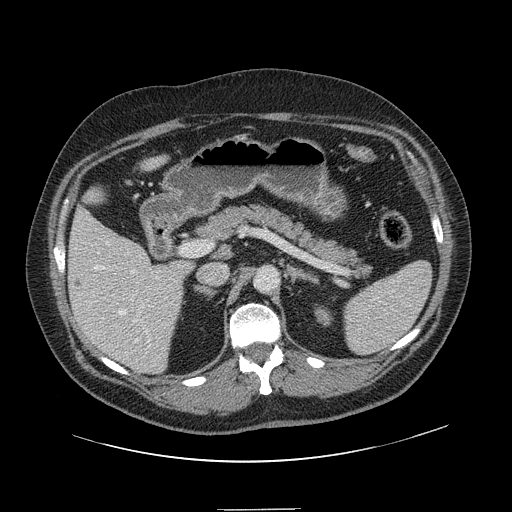
Contrast-enhanced abdominal CT, one axial slice; slice 76 of 154 in the series (ordered by position); intravenous contrast given; soft-tissue window (W 400 / L 40 HU); 512 × 512 image matrix, field of view 451 × 451 mm. Male patient, age 61 years. Case-level facts recorded for this patient, not image findings: diagnosis: colorectal cancer liver metastases, imaged before liver resection; multiple liver metastases: yes; largest metastasis: 2.6 cm; chemotherapy before resection: no.
Structures marked on this image (manually delineated by an expert):
- hepatic veins: box from (x=94, y=265) to (x=138, y=343) px
- liver: (x=68, y=209)–(x=191, y=372)
- planned liver remnant (the part of the liver to remain after resection): (x=69, y=209)–(x=189, y=365)
- portal vein (with intrahepatic branches): (x=131, y=270)–(x=144, y=322)
- liver metastasis: (x=77, y=281)–(x=83, y=288)